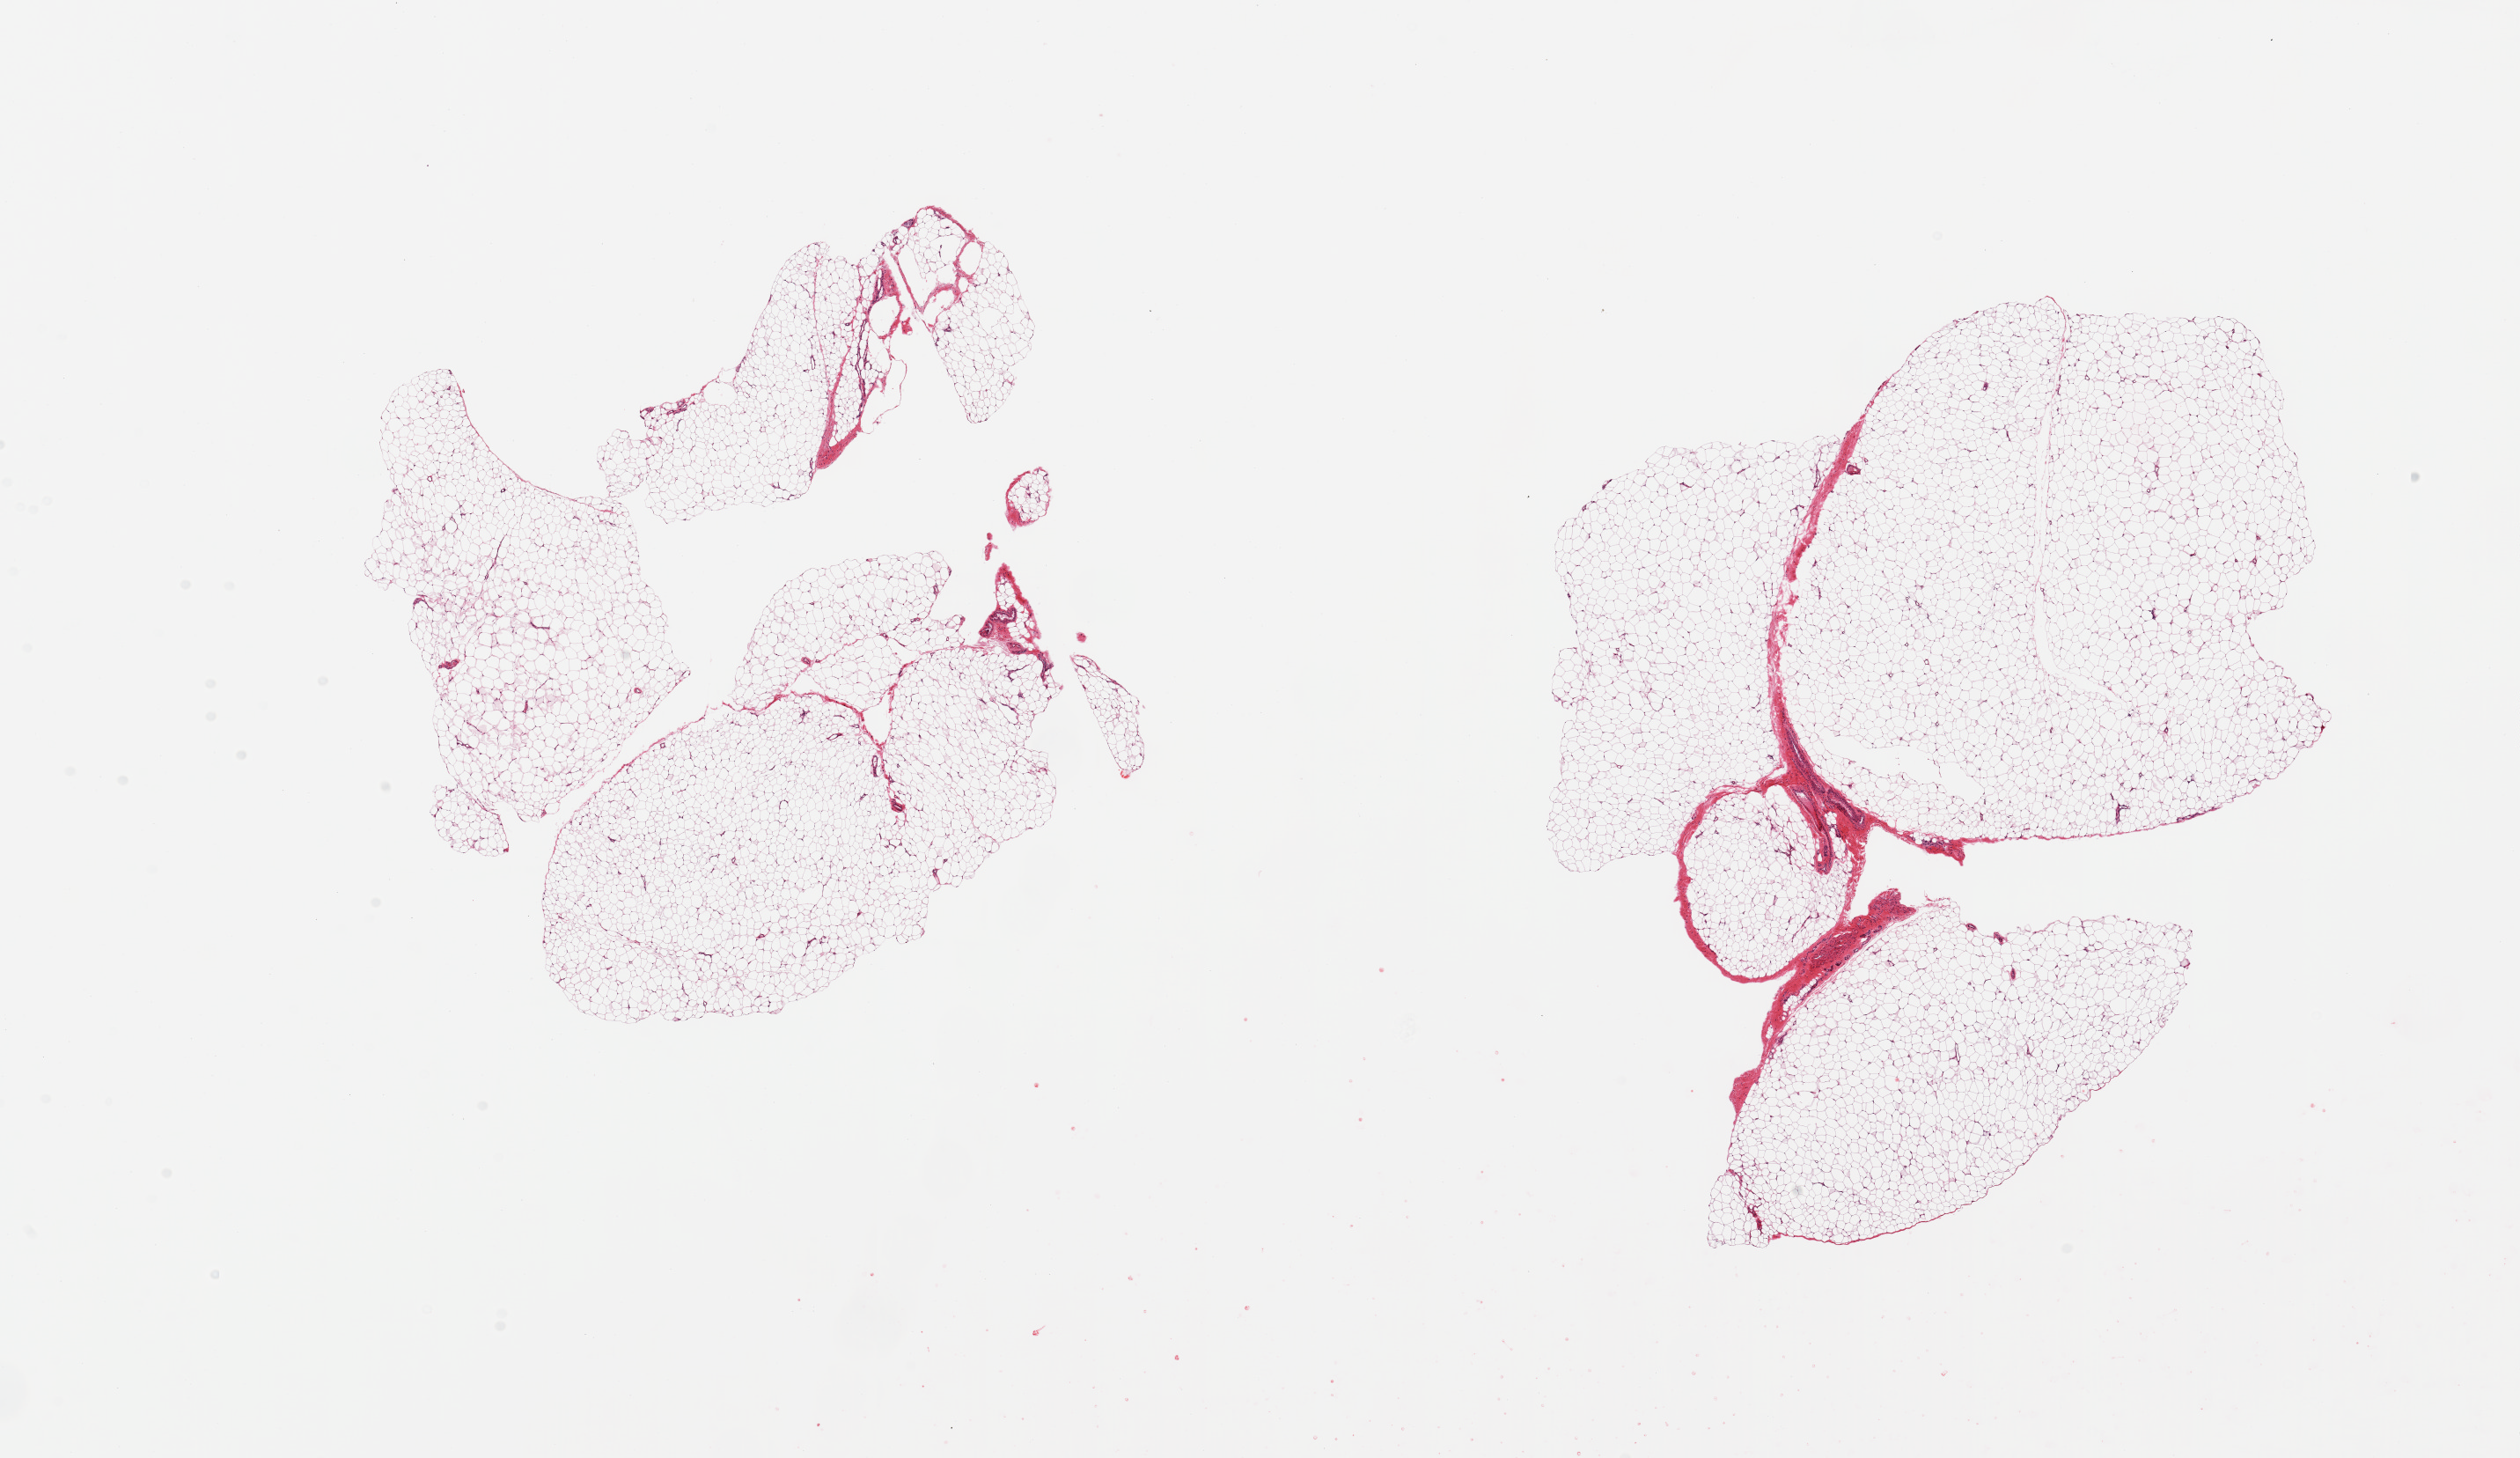
Whole-slide image, H&E stain — whole scanned area (about 22.6 x 13.1 mm, from a 20x scan) shown as a low-resolution overview, PAXgene-fixed paraffin-embedded (PFPE) section, sampled site (target tissue): adipose tissue, tissue donor sample.
Pathologist's review note for this sample: 2 pieces; <2% fibrous content.